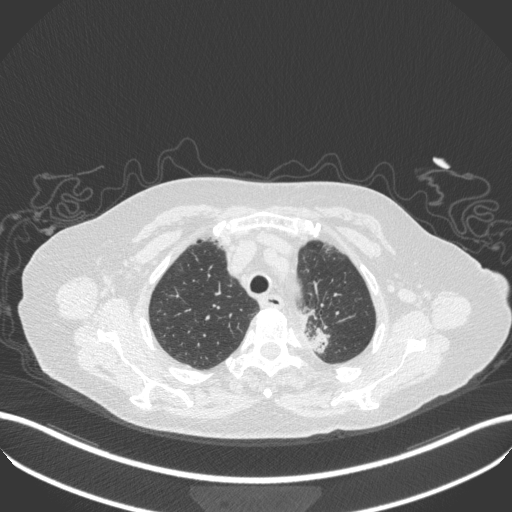
Chest CT, one axial slice. Slice 278 of 353 in the series (ordered by position). 100 kVp. Lung window (W 1500 / L -600 HU). 1 mm slice thickness. 512 × 512 image matrix, field of view 400 × 400 mm. Patient: female, 81 years. Case-level facts recorded for this patient, not image findings: clinical TNM (as recorded): T2a N0 M0.
Annotated regions visible in this slice (bounding box drawn by a radiologist):
- lung tumour (recorded histology: adenocarcinoma): bounding box [x1, y1, x2, y2] px = [276, 302, 332, 356]